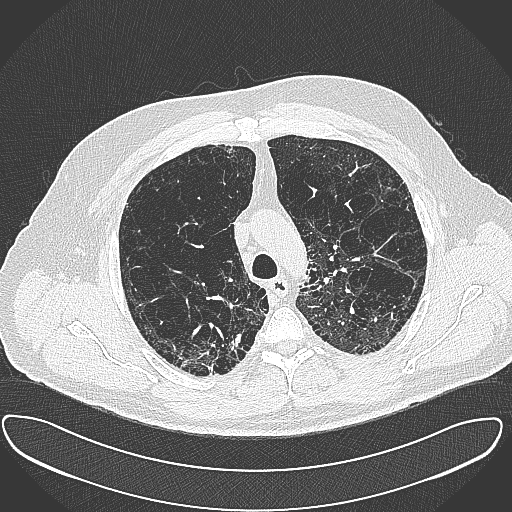
Low-dose screening chest CT, axial slice. Baseline annual screen. Lung window (W 1500 / L -600 HU). 1 mm slice thickness. Lung (sharp) reconstruction kernel (B80f). 512 × 512 image matrix, field of view 408 × 408 mm. Male participant, aged 60 years at enrolment. Current smoker at enrolment.
Expert reader's lesion annotation, bounding box <190,327,252,381> (left, top, right, bottom; pixels). The exam's reader record, not a measurement of the box and not confirmed to be the same lesion: non-calcified nodule or mass ≥4 mm, right upper lobe, 15 × 25 mm, spiculated (stellate) margins, soft tissue attenuation. Lung cancer was diagnosed 32 days after this screen: carcinoma, NOS, right upper lobe, moderately differentiated (G2), stage IB (AJCC 6th edition), 35 mm at pathology.